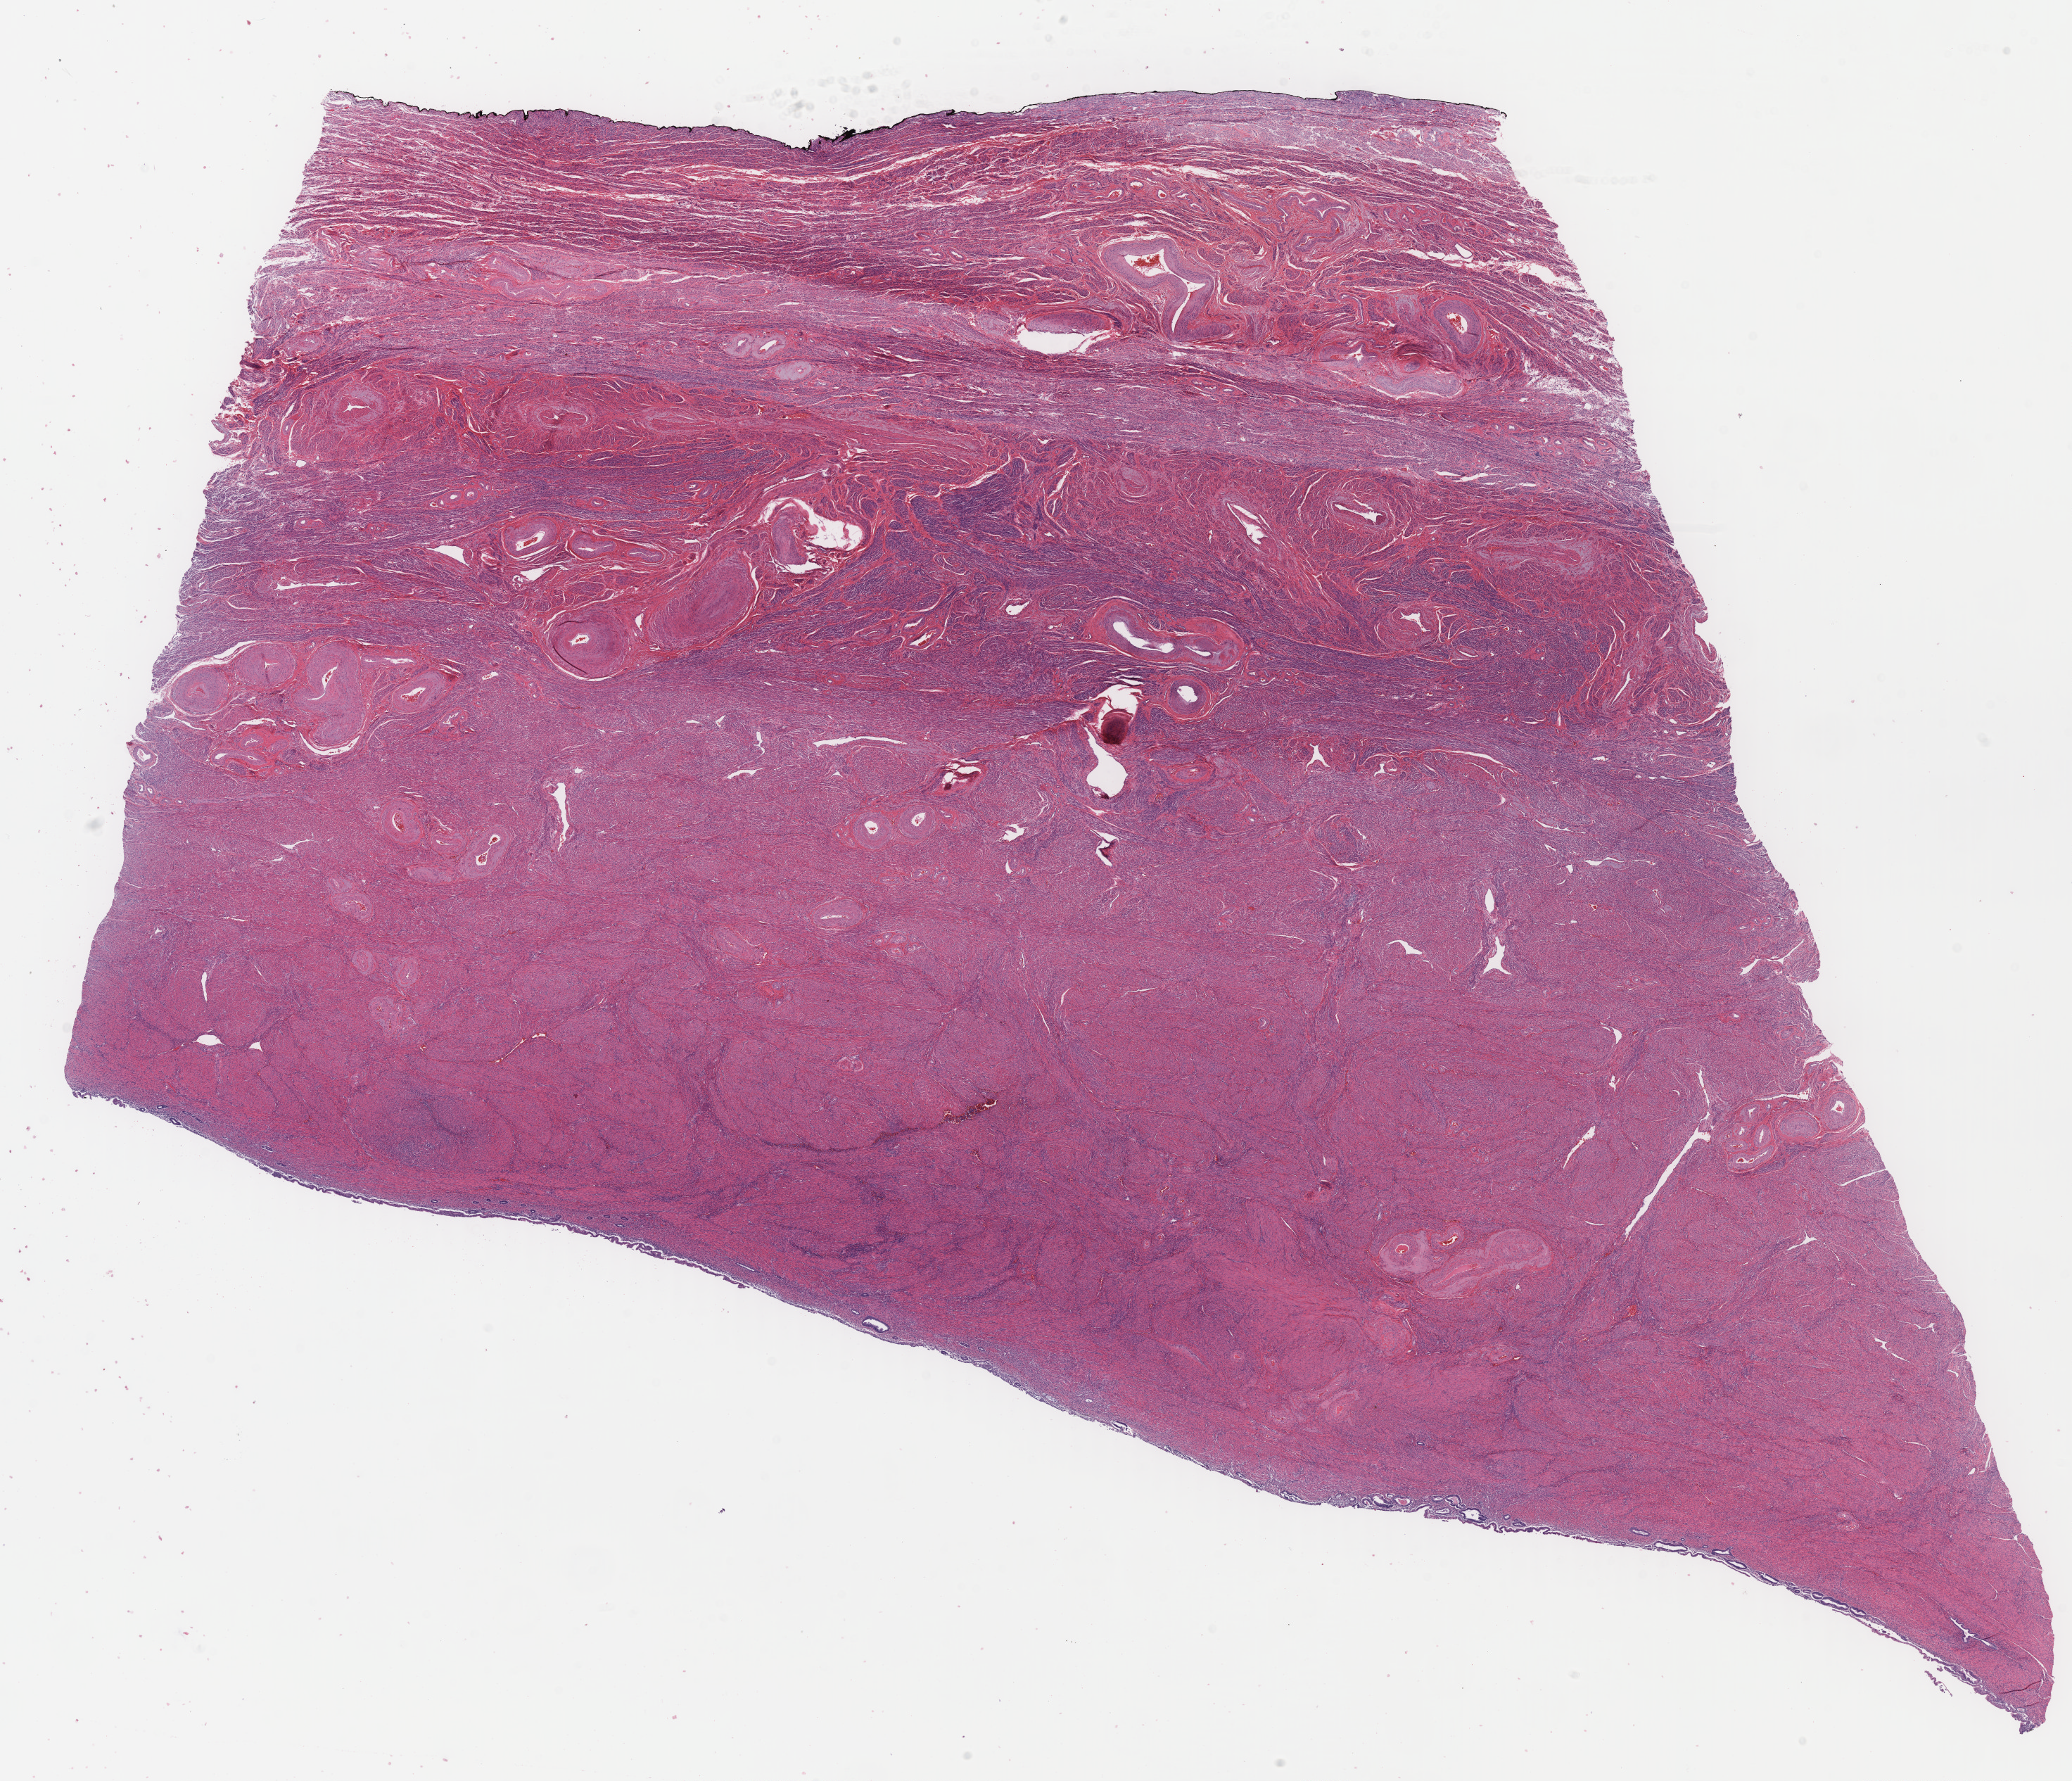
Whole-slide image, hematoxylin and eosin (H&E) stain — shown as a low-resolution overview of the whole scanned area (about 23.3 x 20.0 mm), frozen section (tissue freezing medium), specimen: non-tumor (normal tissue) sample from a patient with carcinoma, undifferentiated, NOS, anatomic site: body of uterus. Patient sex: female. Composition of this section per pathologist review: tumor cells 0%, tumor nuclei 0%, stromal cells 97%, necrosis 0%, normal cells 3%. Infiltration values recorded for this section: lymphocyte infiltration 3%, monocyte infiltration 1%, neutrophil infiltration 0%.
• this section: non-tumor tissue sample; the patient's diagnosis is given above